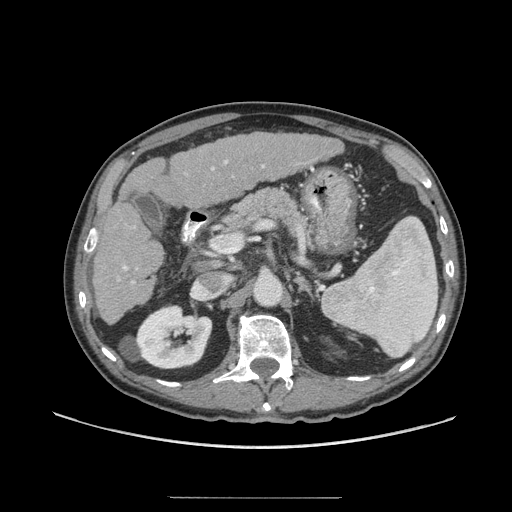
Contrast-enhanced abdominal CT (liver protocol), one axial slice. Position 33 of 71 along the scan axis. Reconstruction kernel STANDARD. Soft-tissue window (W 400 / L 40 HU). 512 × 512 image matrix, field of view 400 × 400 mm. From the clinical record (not read from this slice): diagnosis: hepatocellular carcinoma (patient treated with transarterial chemoembolisation; whether this scan precedes or follows treatment is not stated here); TNM stage (as recorded): Stage-I; Child-Pugh class: A; tumour differentiation: well differentiated.
Outlined on this slice (semi-automatic segmentation, software-assisted and operator-edited):
- liver parenchyma outside the tumour (the mass and vessels are separate outlines, so this box may not span the whole liver): box from (x=92, y=132) to (x=341, y=324) px
- liver vessels: (x=118, y=160)–(x=265, y=284)